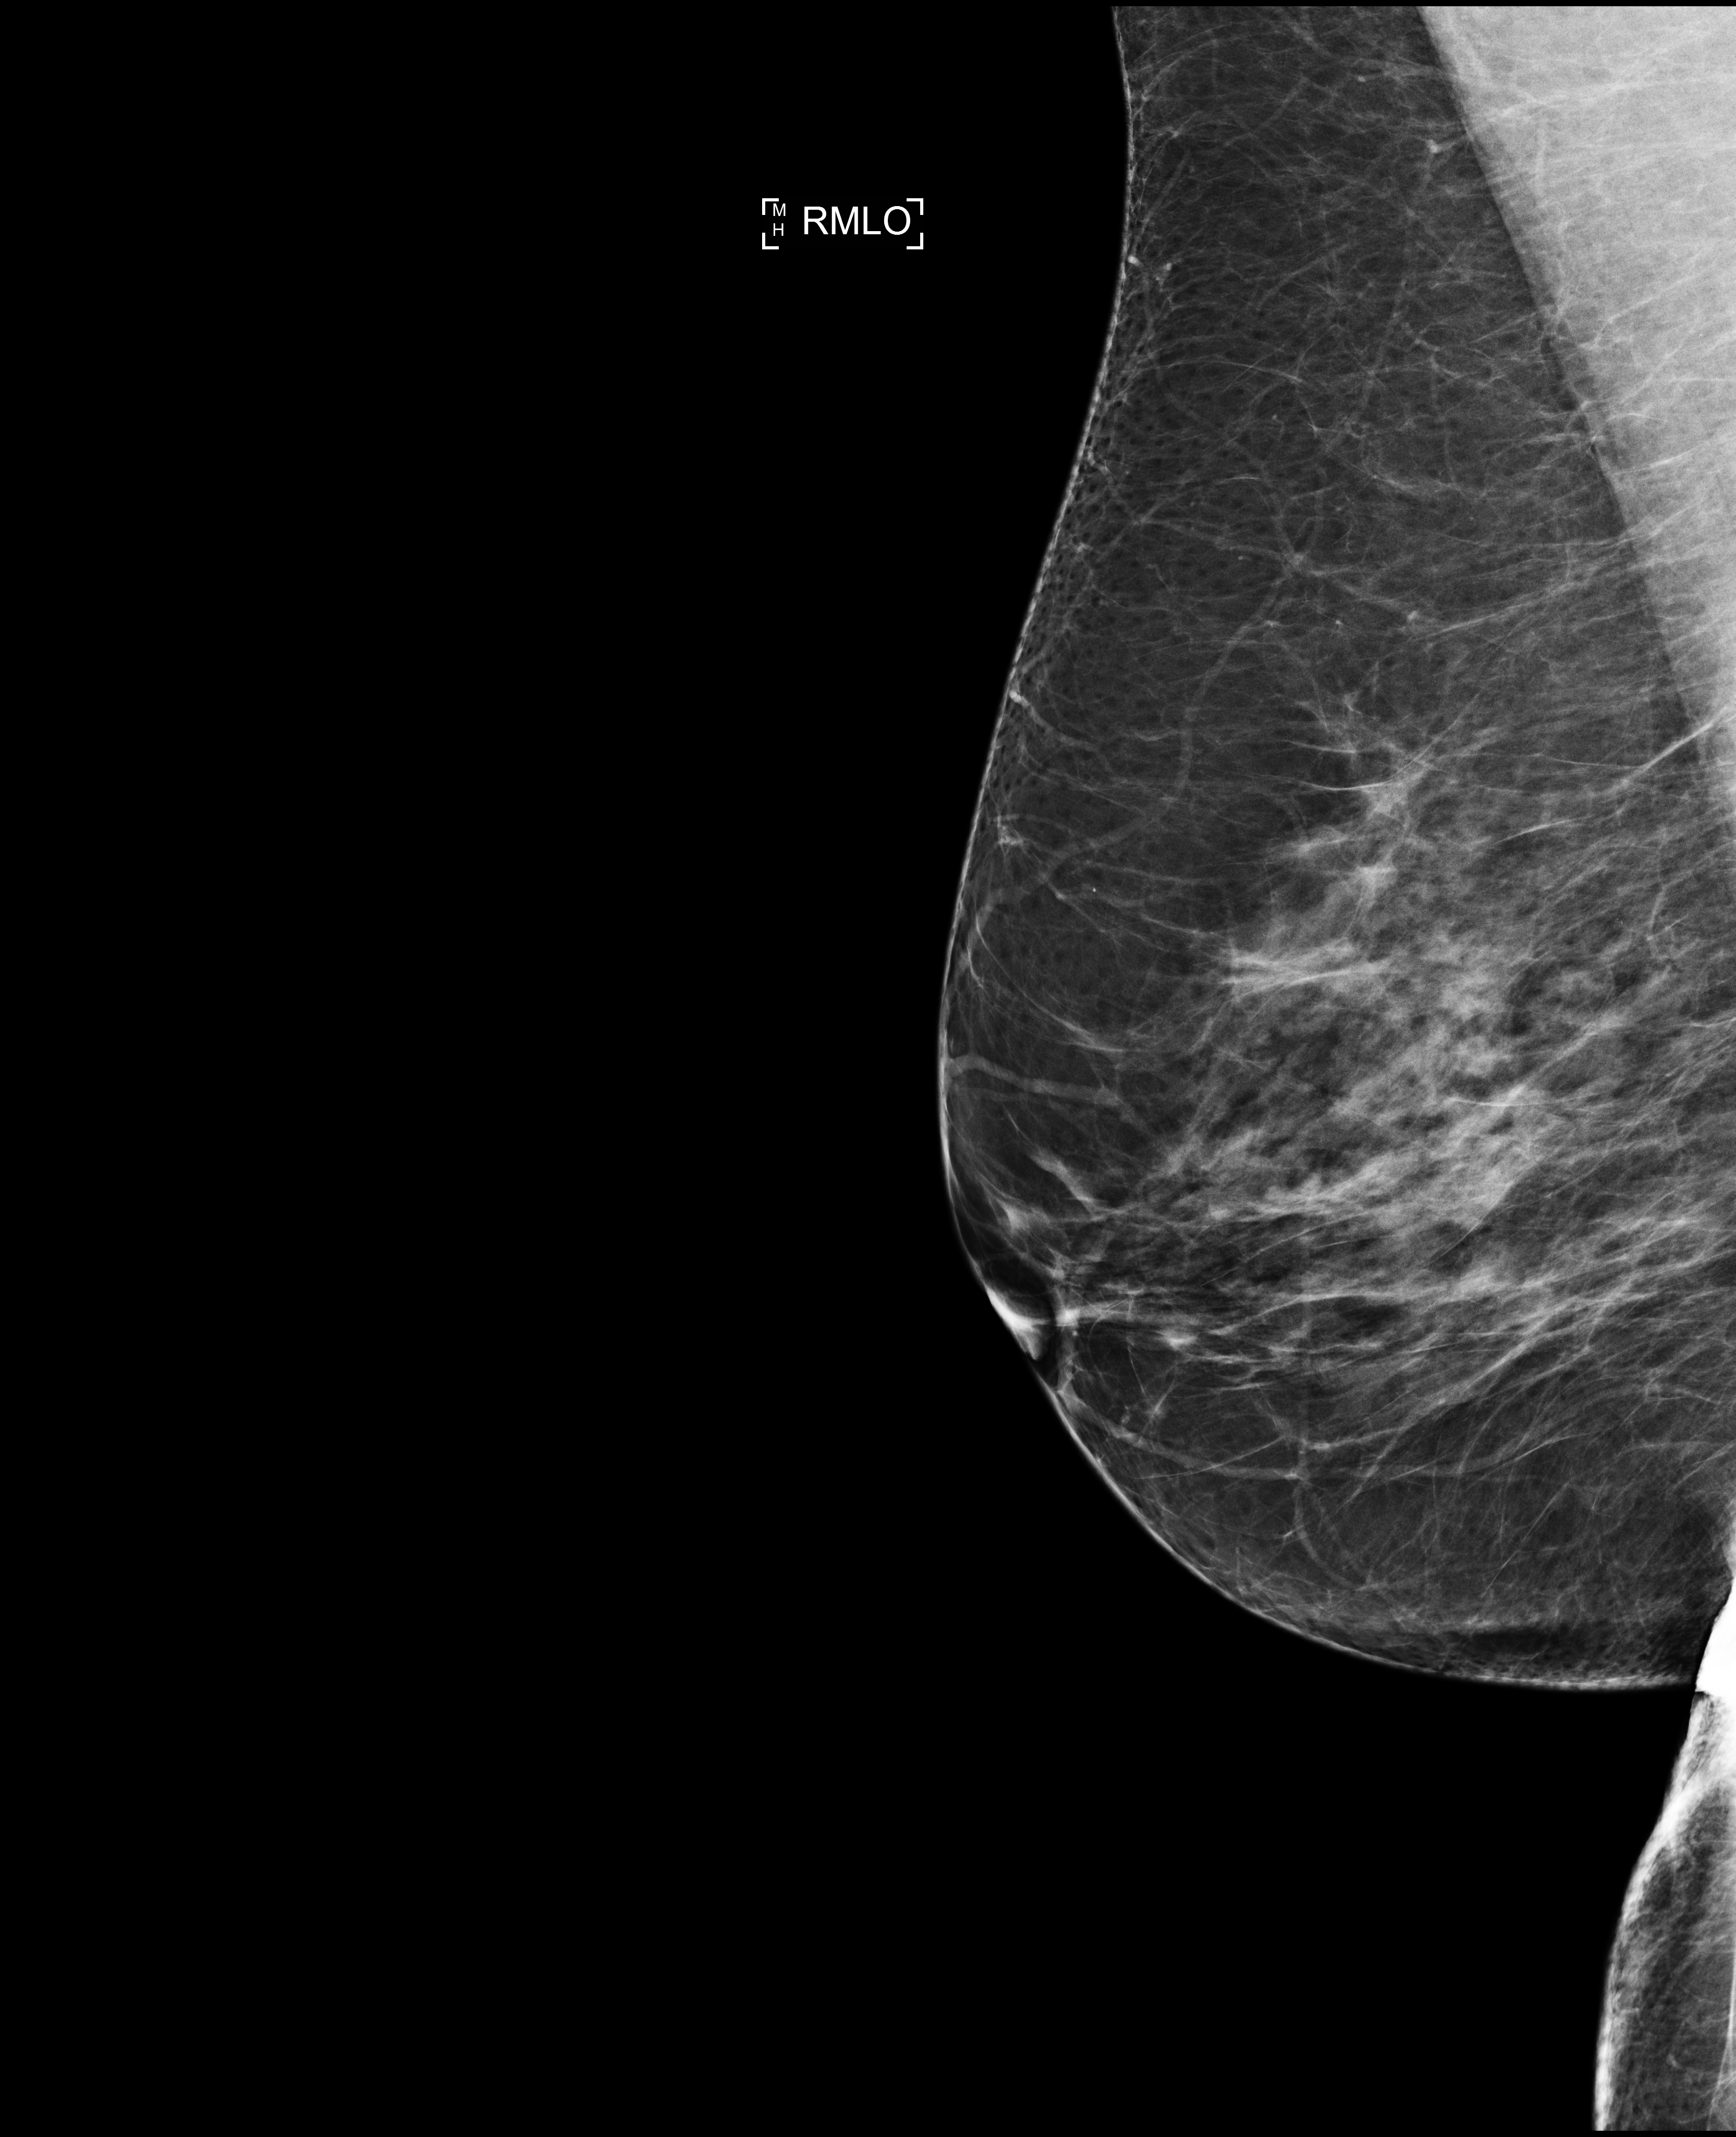
Annual screening mammography examination; system: Selenia Dimensions. Patient aged 57 years (female).
Image type: full-field digital mammogram. Breast: right. Projection: MLO view.